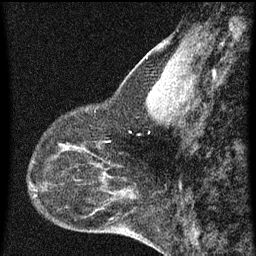
Breast MRI (dynamic contrast-enhanced), one sagittal slice. Slice 23 of 60 in the series (ordered by position). Dynamic contrast-enhanced series, image 2 of 3 at this slice position (ordered by acquisition). 1.5 T. TE 4.2 ms, TR 8 ms. 256 × 256 image matrix, field of view 180 × 180 mm. Female patient, age 44 years.
Outlined on this slice (semi-automatic segmentation, software-assisted and operator-edited):
- analysis volume of interest (the breast-tissue region the enhancement analysis was run in; not a lesion): bounding box [x1, y1, x2, y2] px = [49, 128, 95, 169]
- tumour enhancement mask (voxels above the 70 % enhancement threshold inside the analysis volume of interest): [59, 146, 85, 149]